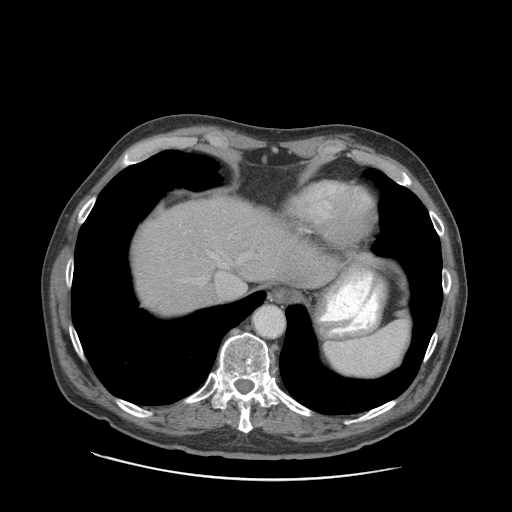
Contrast-enhanced abdominal CT (liver protocol), one axial slice. Position 76 of 89 along the scan axis. Reconstruction kernel STANDARD. Soft-tissue window (W 400 / L 40 HU). 2.5 mm slice thickness. 512 × 512 image matrix. Case-level facts recorded for this patient, not image findings: diagnosis: hepatocellular carcinoma (patient treated with transarterial chemoembolisation; whether this scan precedes or follows treatment is not stated here); TNM stage (as recorded): Stage-I; Child-Pugh class: A; tumour differentiation: moderately differentiated; tumour nodularity: uninodular.
Annotated regions visible in this slice (semi-automatic segmentation, software-assisted and operator-edited):
- liver parenchyma outside the tumour (the mass and vessels are separate outlines, so this box may not span the whole liver): bounding box <134,198,338,314> (left, top, right, bottom; pixels)
- liver vessels: <210,253,242,285>